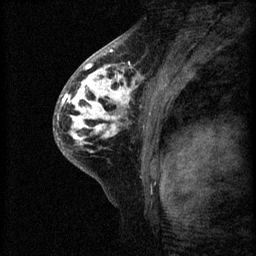
Breast MRI (dynamic contrast-enhanced), one sagittal slice. Slice 39 of 60 in the series (ordered by position). 3 images stored at this slice position (order not interpretable as contrast timing). 1.5 T. TE 4.2 ms, TR 8.2 ms. 256 × 256 image matrix, field of view 180 × 180 mm. Female patient, age 41 years.
Annotated regions visible in this slice (semi-automatic segmentation, software-assisted and operator-edited):
- analysis volume of interest (the breast-tissue region the enhancement analysis was run in; not a lesion): bounding box (x1, y1, x2, y2) in pixels: (53, 62, 160, 175)
- tumour enhancement mask (voxels above the 70 % enhancement threshold inside the analysis volume of interest): (57, 62, 151, 153)